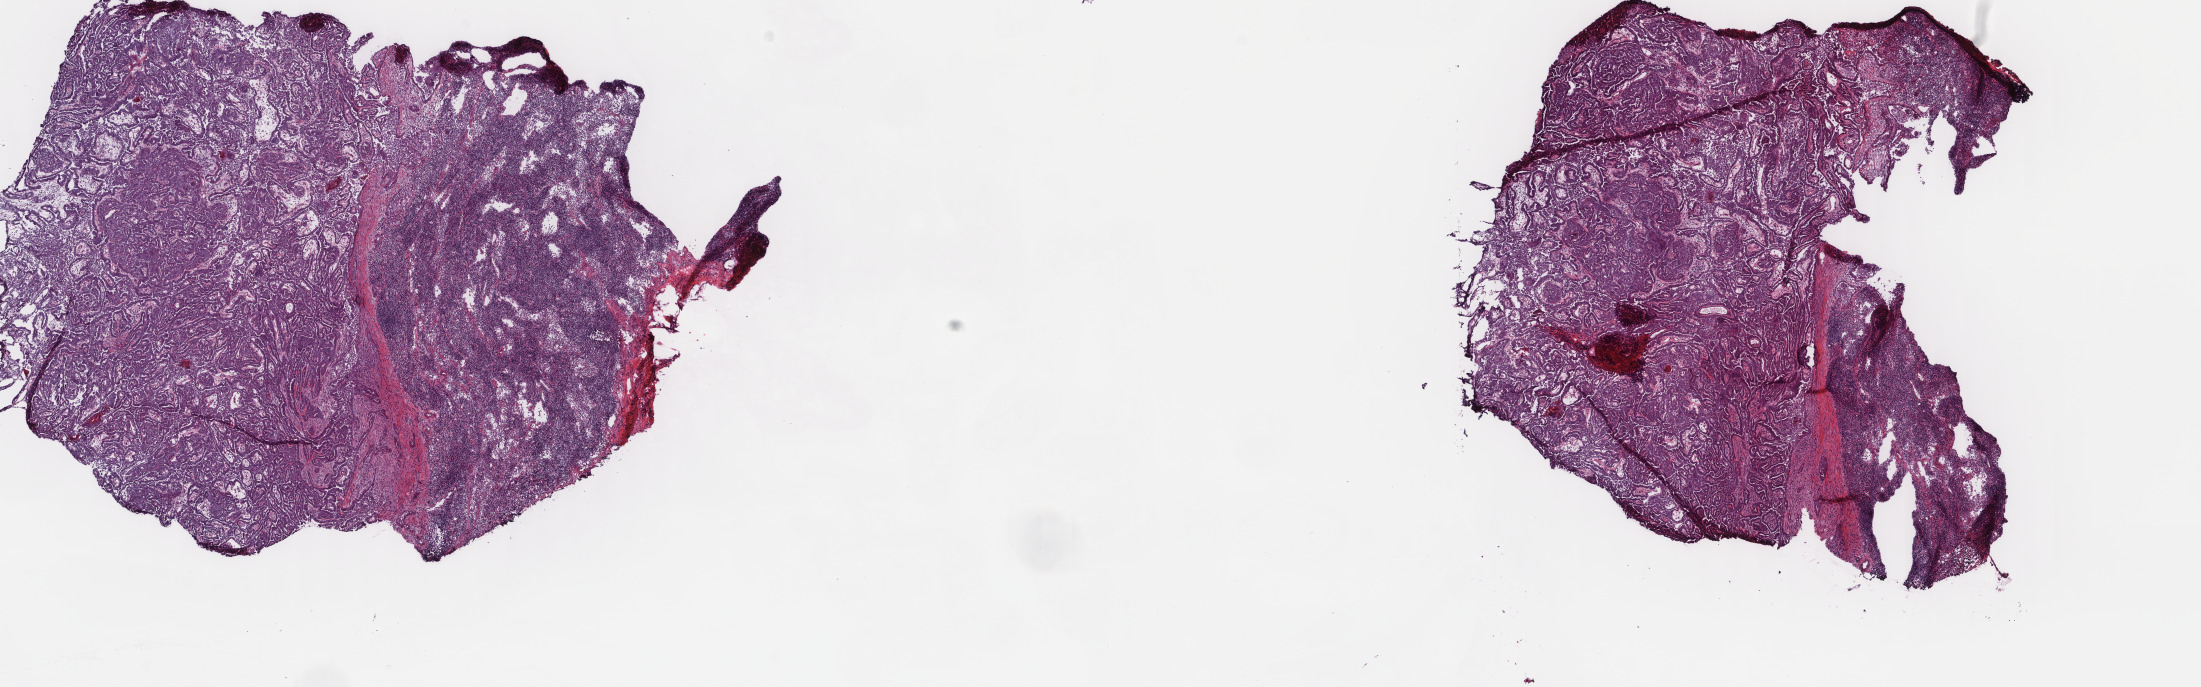
Hematoxylin and eosin (H&E) stained whole-slide image — shown as a low-resolution overview of the whole scanned area (about 17.5 x 5.5 mm), frozen section, thyroid, primary tumour sample. Male patient; age at initial diagnosis 49 years. Pathologist review of this section (percent, as recorded): tumour cells 60%, tumour nuclei 60%, normal cells 0%, stromal cells 40%, necrosis 0%. Inflammatory infiltration, as recorded: lymphocyte infiltration 40%, monocyte infiltration 10%, neutrophil infiltration 0%.
Lymph nodes positive (case pathology): 3 of 5 examined. Laterality: left. AJCC pathologic stage: IVA (7th edition). Pathologic diagnosis: Papillary adenocarcinoma, NOS (thyroid gland).